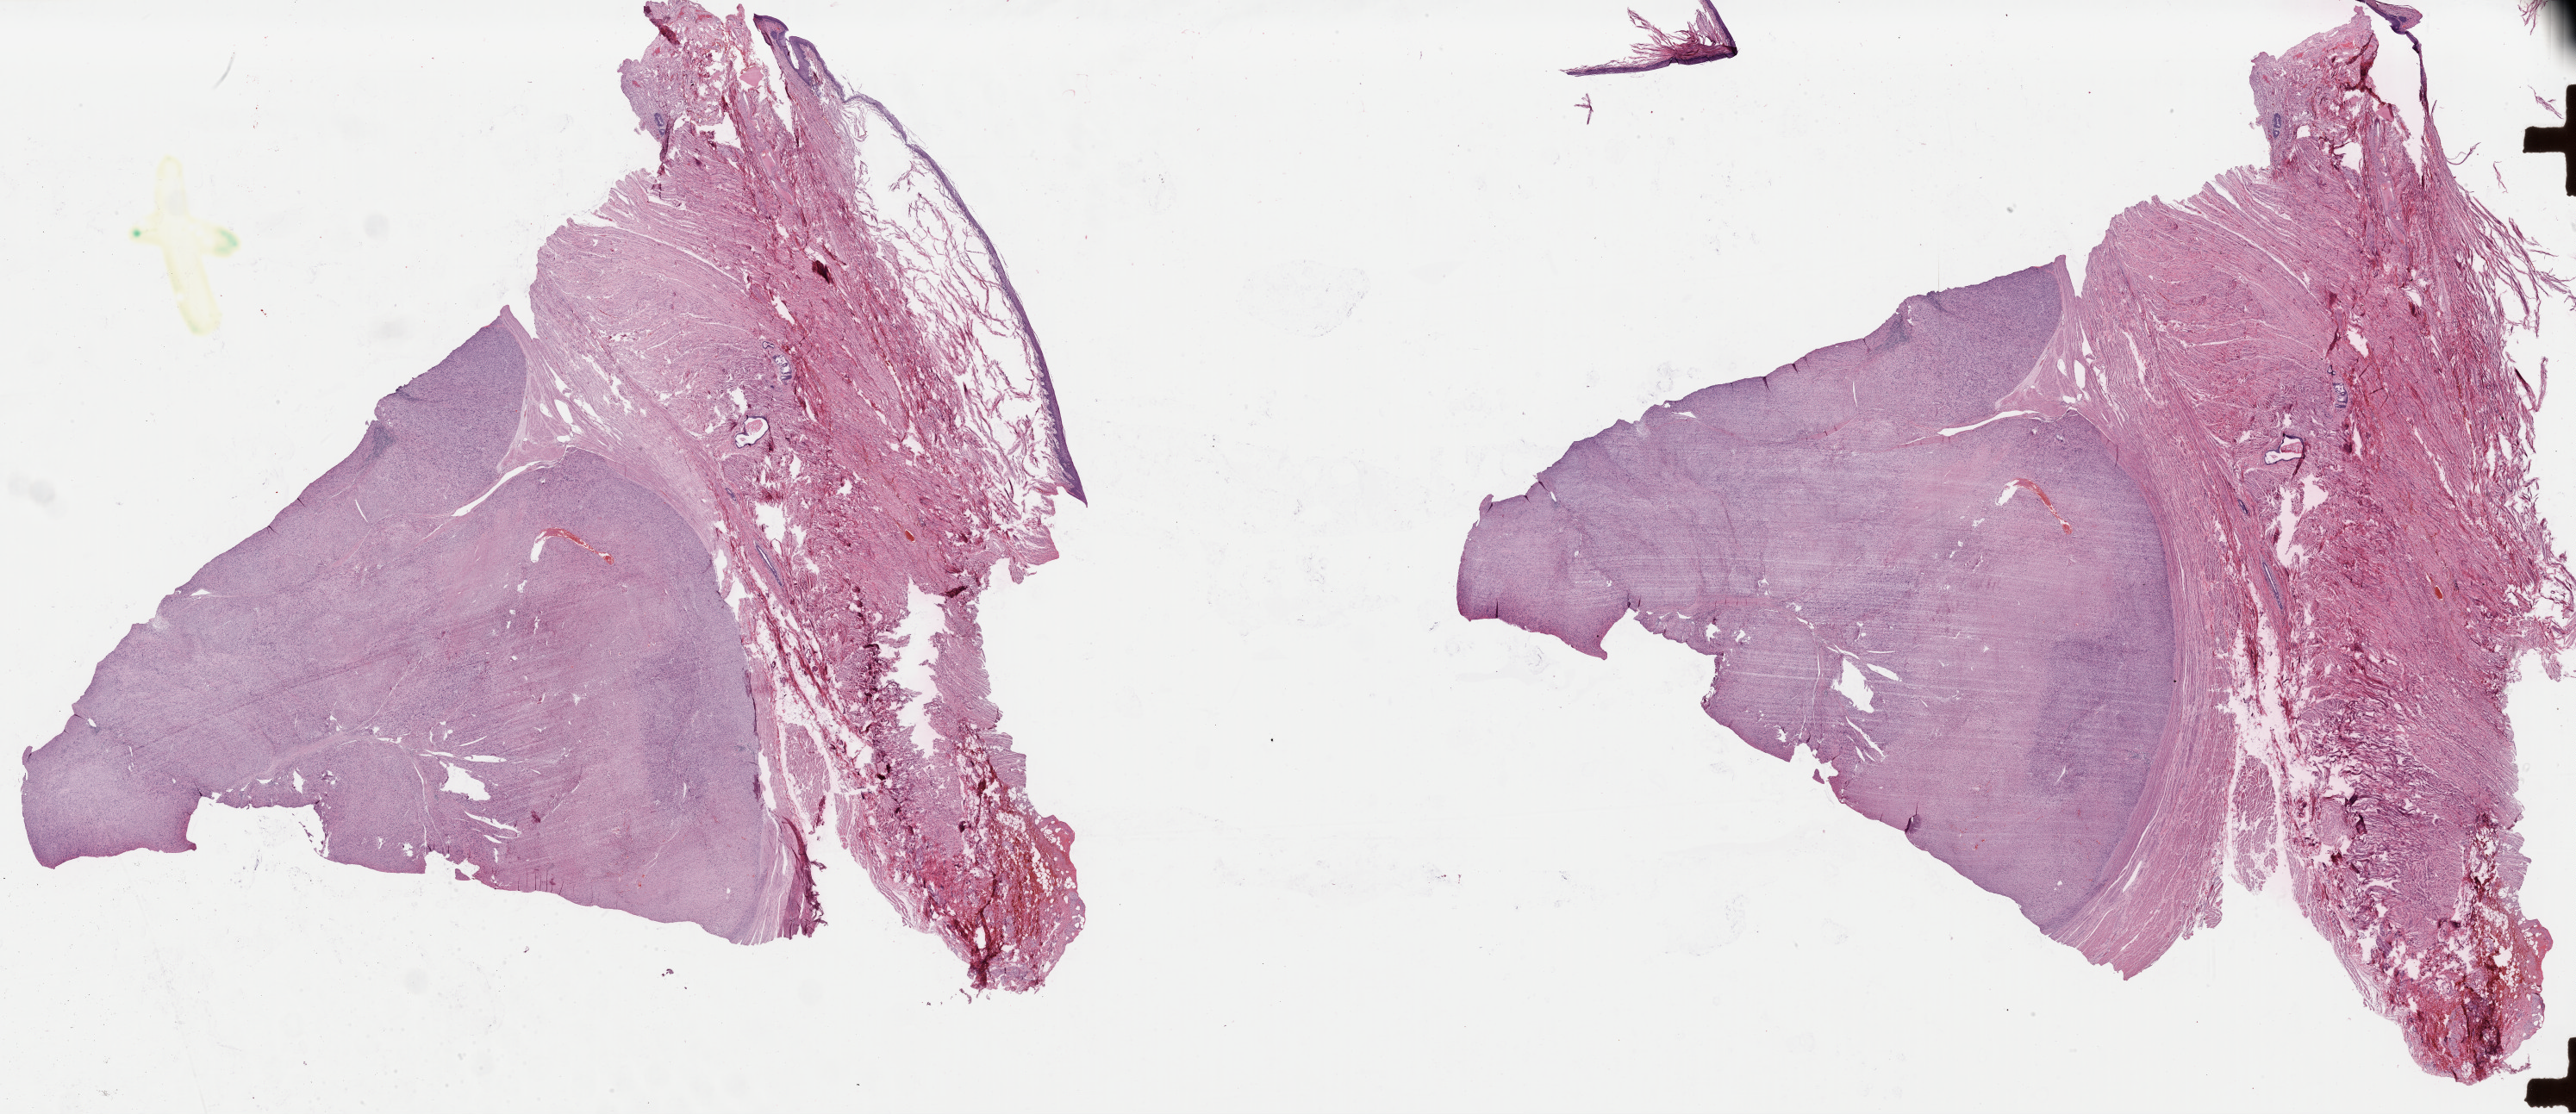
Whole-slide histology image, Hematoxylin and eosin (H&E) stained, a low-resolution overview of the entire scanned area, about 47.2 x 20.4 mm. Formalin-fixed paraffin-embedded (FFPE) diagnostic section. Retroperitoneum and peritoneum, primary tumour sample. Female, age 57 years at initial diagnosis.
- histologic diagnosis: Leiomyosarcoma, NOS